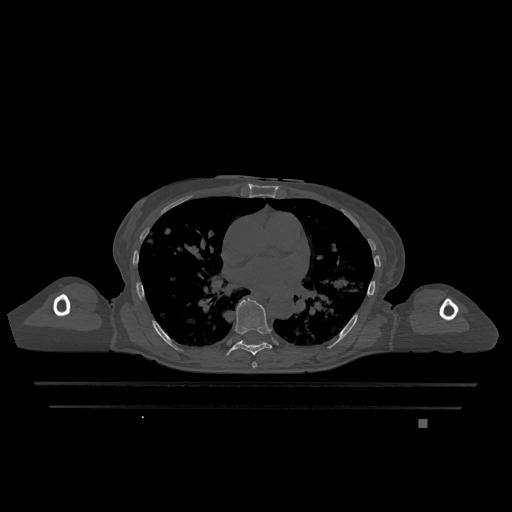
CT including the spine, one axial slice. Position 735 of 1317 along the scan axis. Bone window (W 1800 / L 400 HU). 0.5 mm slice thickness. 512 × 512 image matrix. Female patient, age 74 years. Case-level facts recorded for this patient, not image findings: primary cancer: lung.
Structures marked on this image (semi-automatic segmentation, software-assisted and operator-edited):
- T6 vertebra: box from (x=252, y=362) to (x=257, y=368) px
- T7 vertebra: (x=225, y=298)–(x=272, y=356)